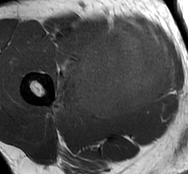
MRI of an extremity soft-tissue mass, one axial slice; position 37 of 93 along the scan axis; MR volume resampled by the dataset authors to the PET/CT grid (not the native acquisition matrix); 3.27 mm slice thickness; 188 × 174 image matrix, field of view 184 × 170 mm. Male patient. Case-level facts recorded for this patient, not image findings: histological type: undifferentiated - pleiomorphic; grade: high; site of the primary tumour: right thigh.
Annotated regions visible in this slice (expert contour drawn on MRI and transferred to this co-registered scan by the dataset authors):
- gross tumour volume including surrounding oedema: bounding box [x1, y1, x2, y2] px = [54, 21, 176, 118]
- gross tumour volume (mass): [72, 24, 174, 118]